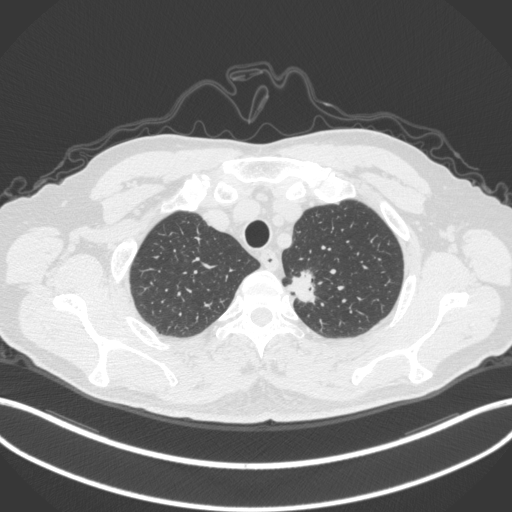
Chest CT, one axial slice. Slice 322 of 382 in the series (ordered by position). 120 kVp. Lung window (W 1500 / L -600 HU). 1 mm slice thickness. 512 × 512 image matrix, field of view 400 × 400 mm. Patient: male, 64 years. Case-level facts recorded for this patient, not image findings: clinical TNM (as recorded): T1c N0 M0.
Annotated regions visible in this slice (bounding box drawn by a radiologist):
- lung tumour (recorded histology: adenocarcinoma): box from (x=282, y=264) to (x=322, y=307) px